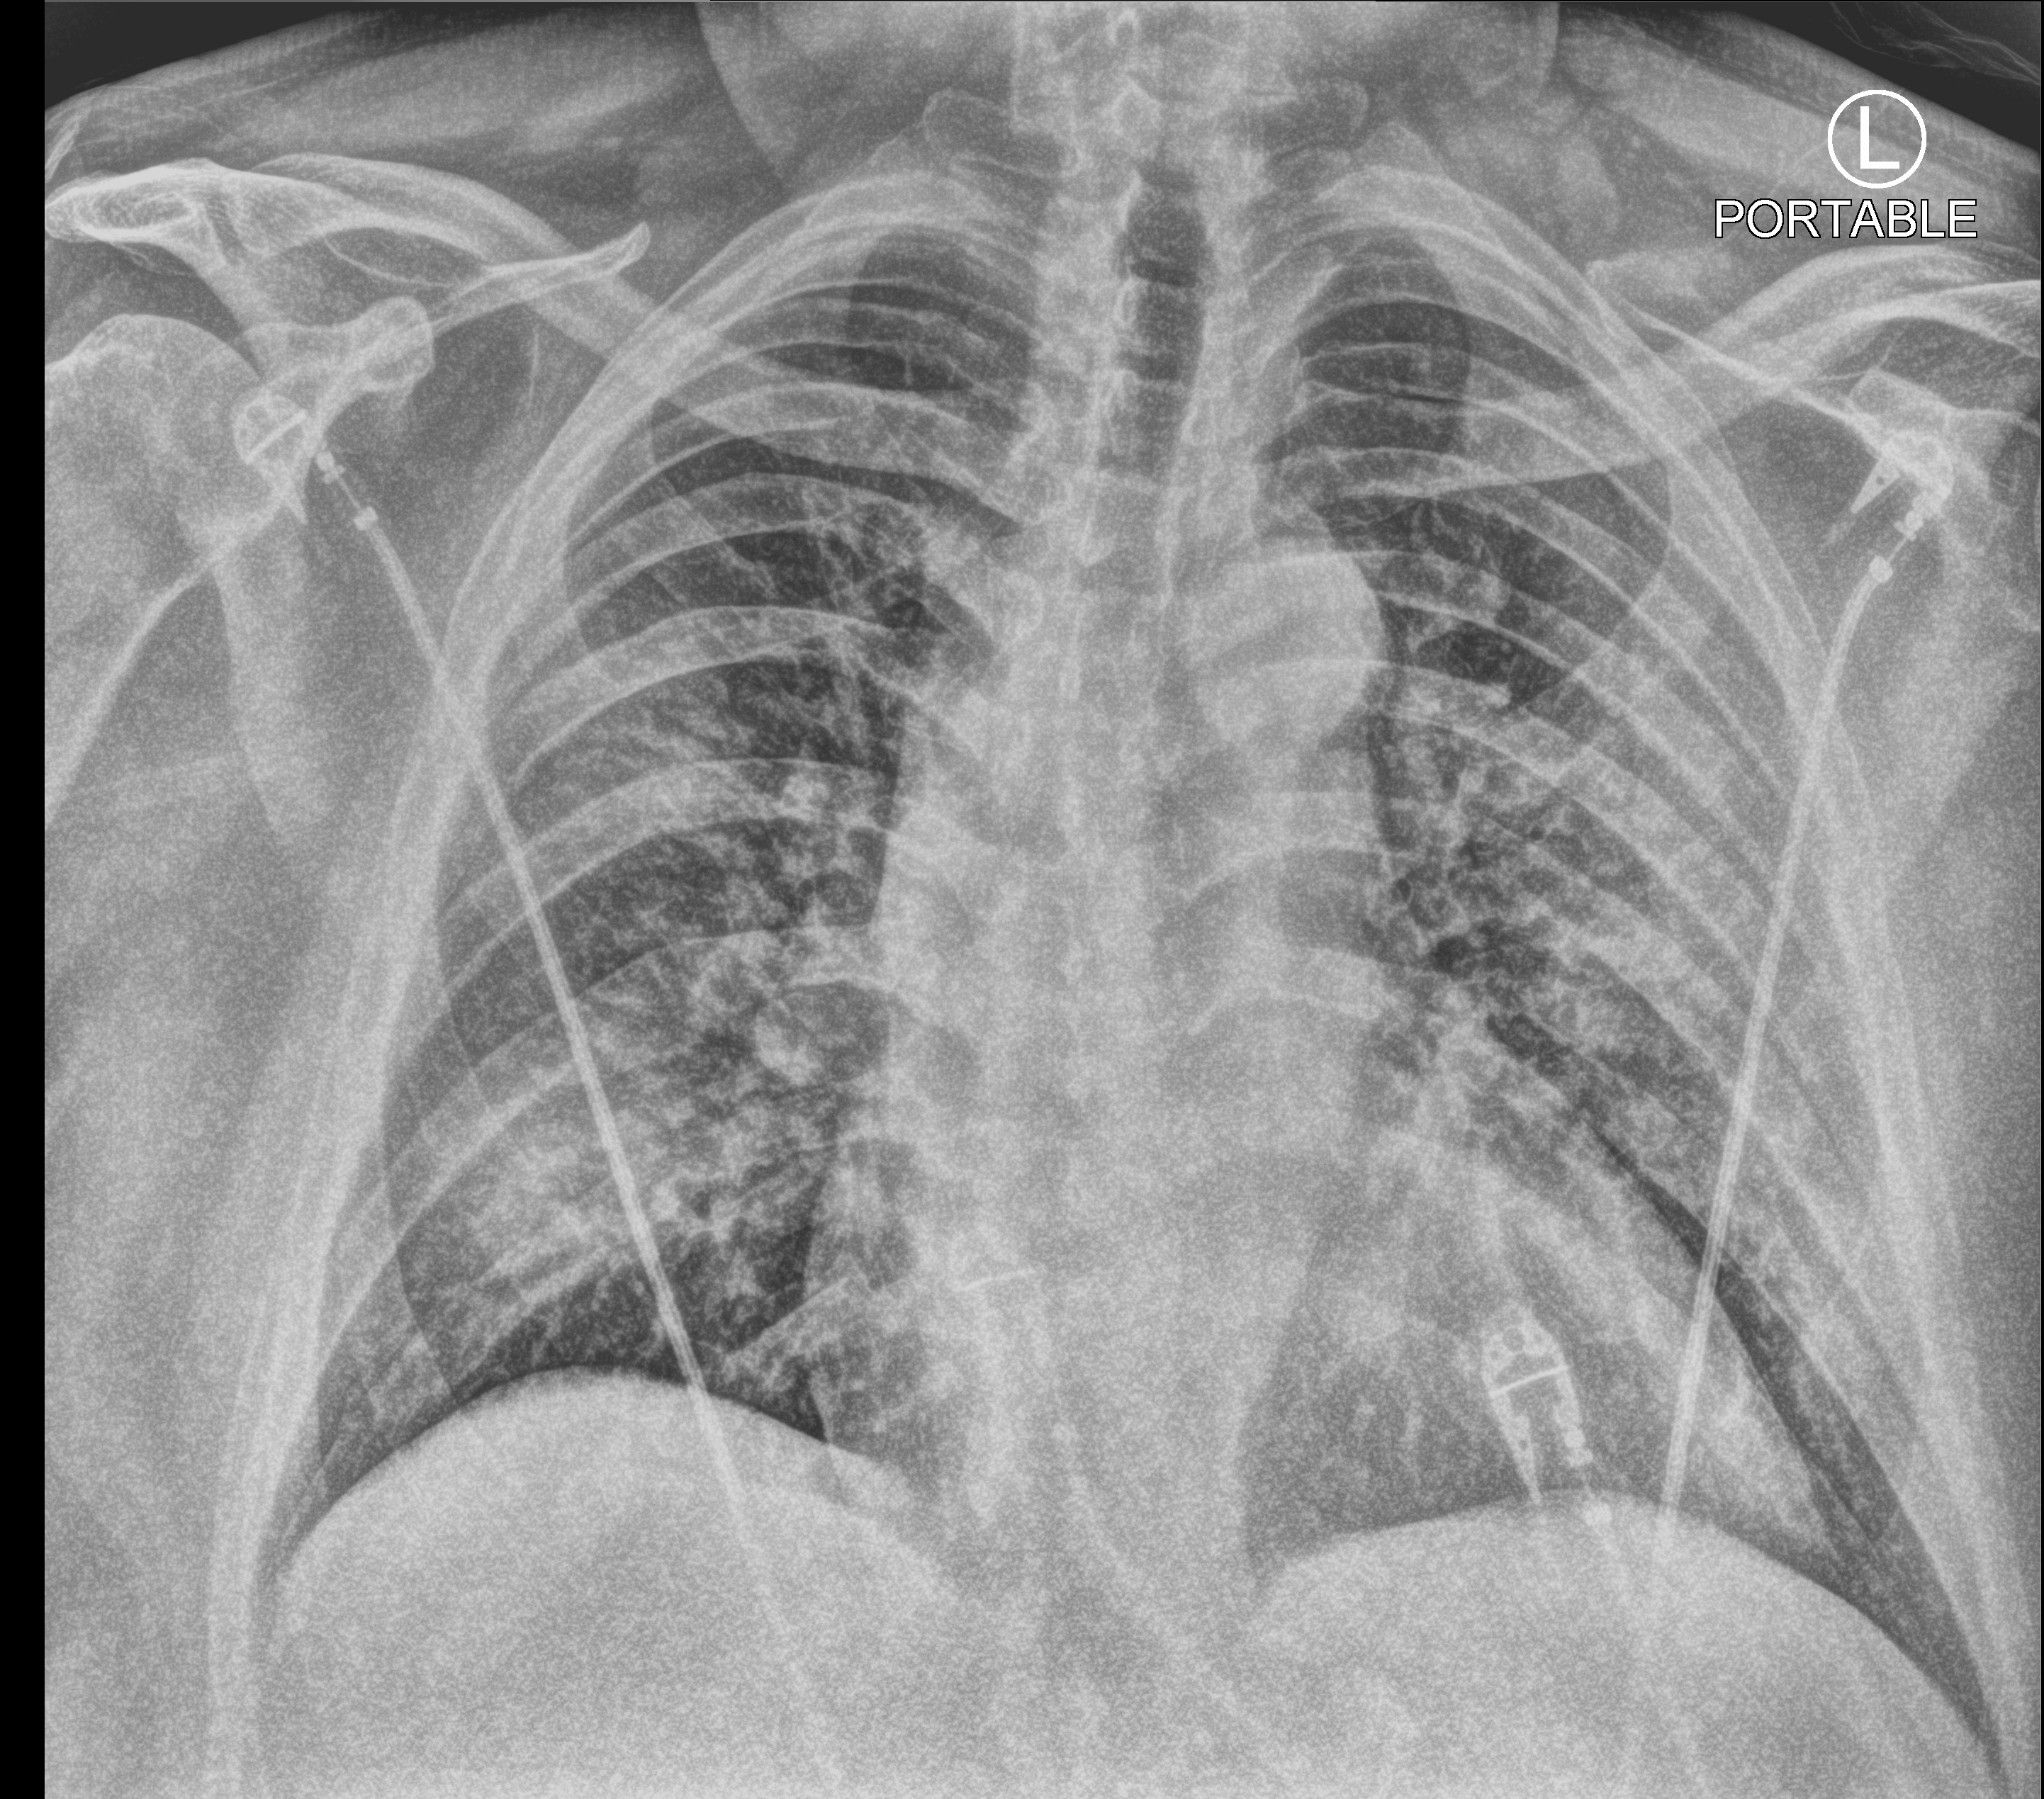
Bedside chest radiograph (computed radiography), anteroposterior (AP) projection. Male patient hospitalised with COVID-19, age 60–74 years.
From the hospital-stay record, not from the radiograph (when in the stay this image was taken is not recorded): mechanically ventilated during this hospital stay: yes.